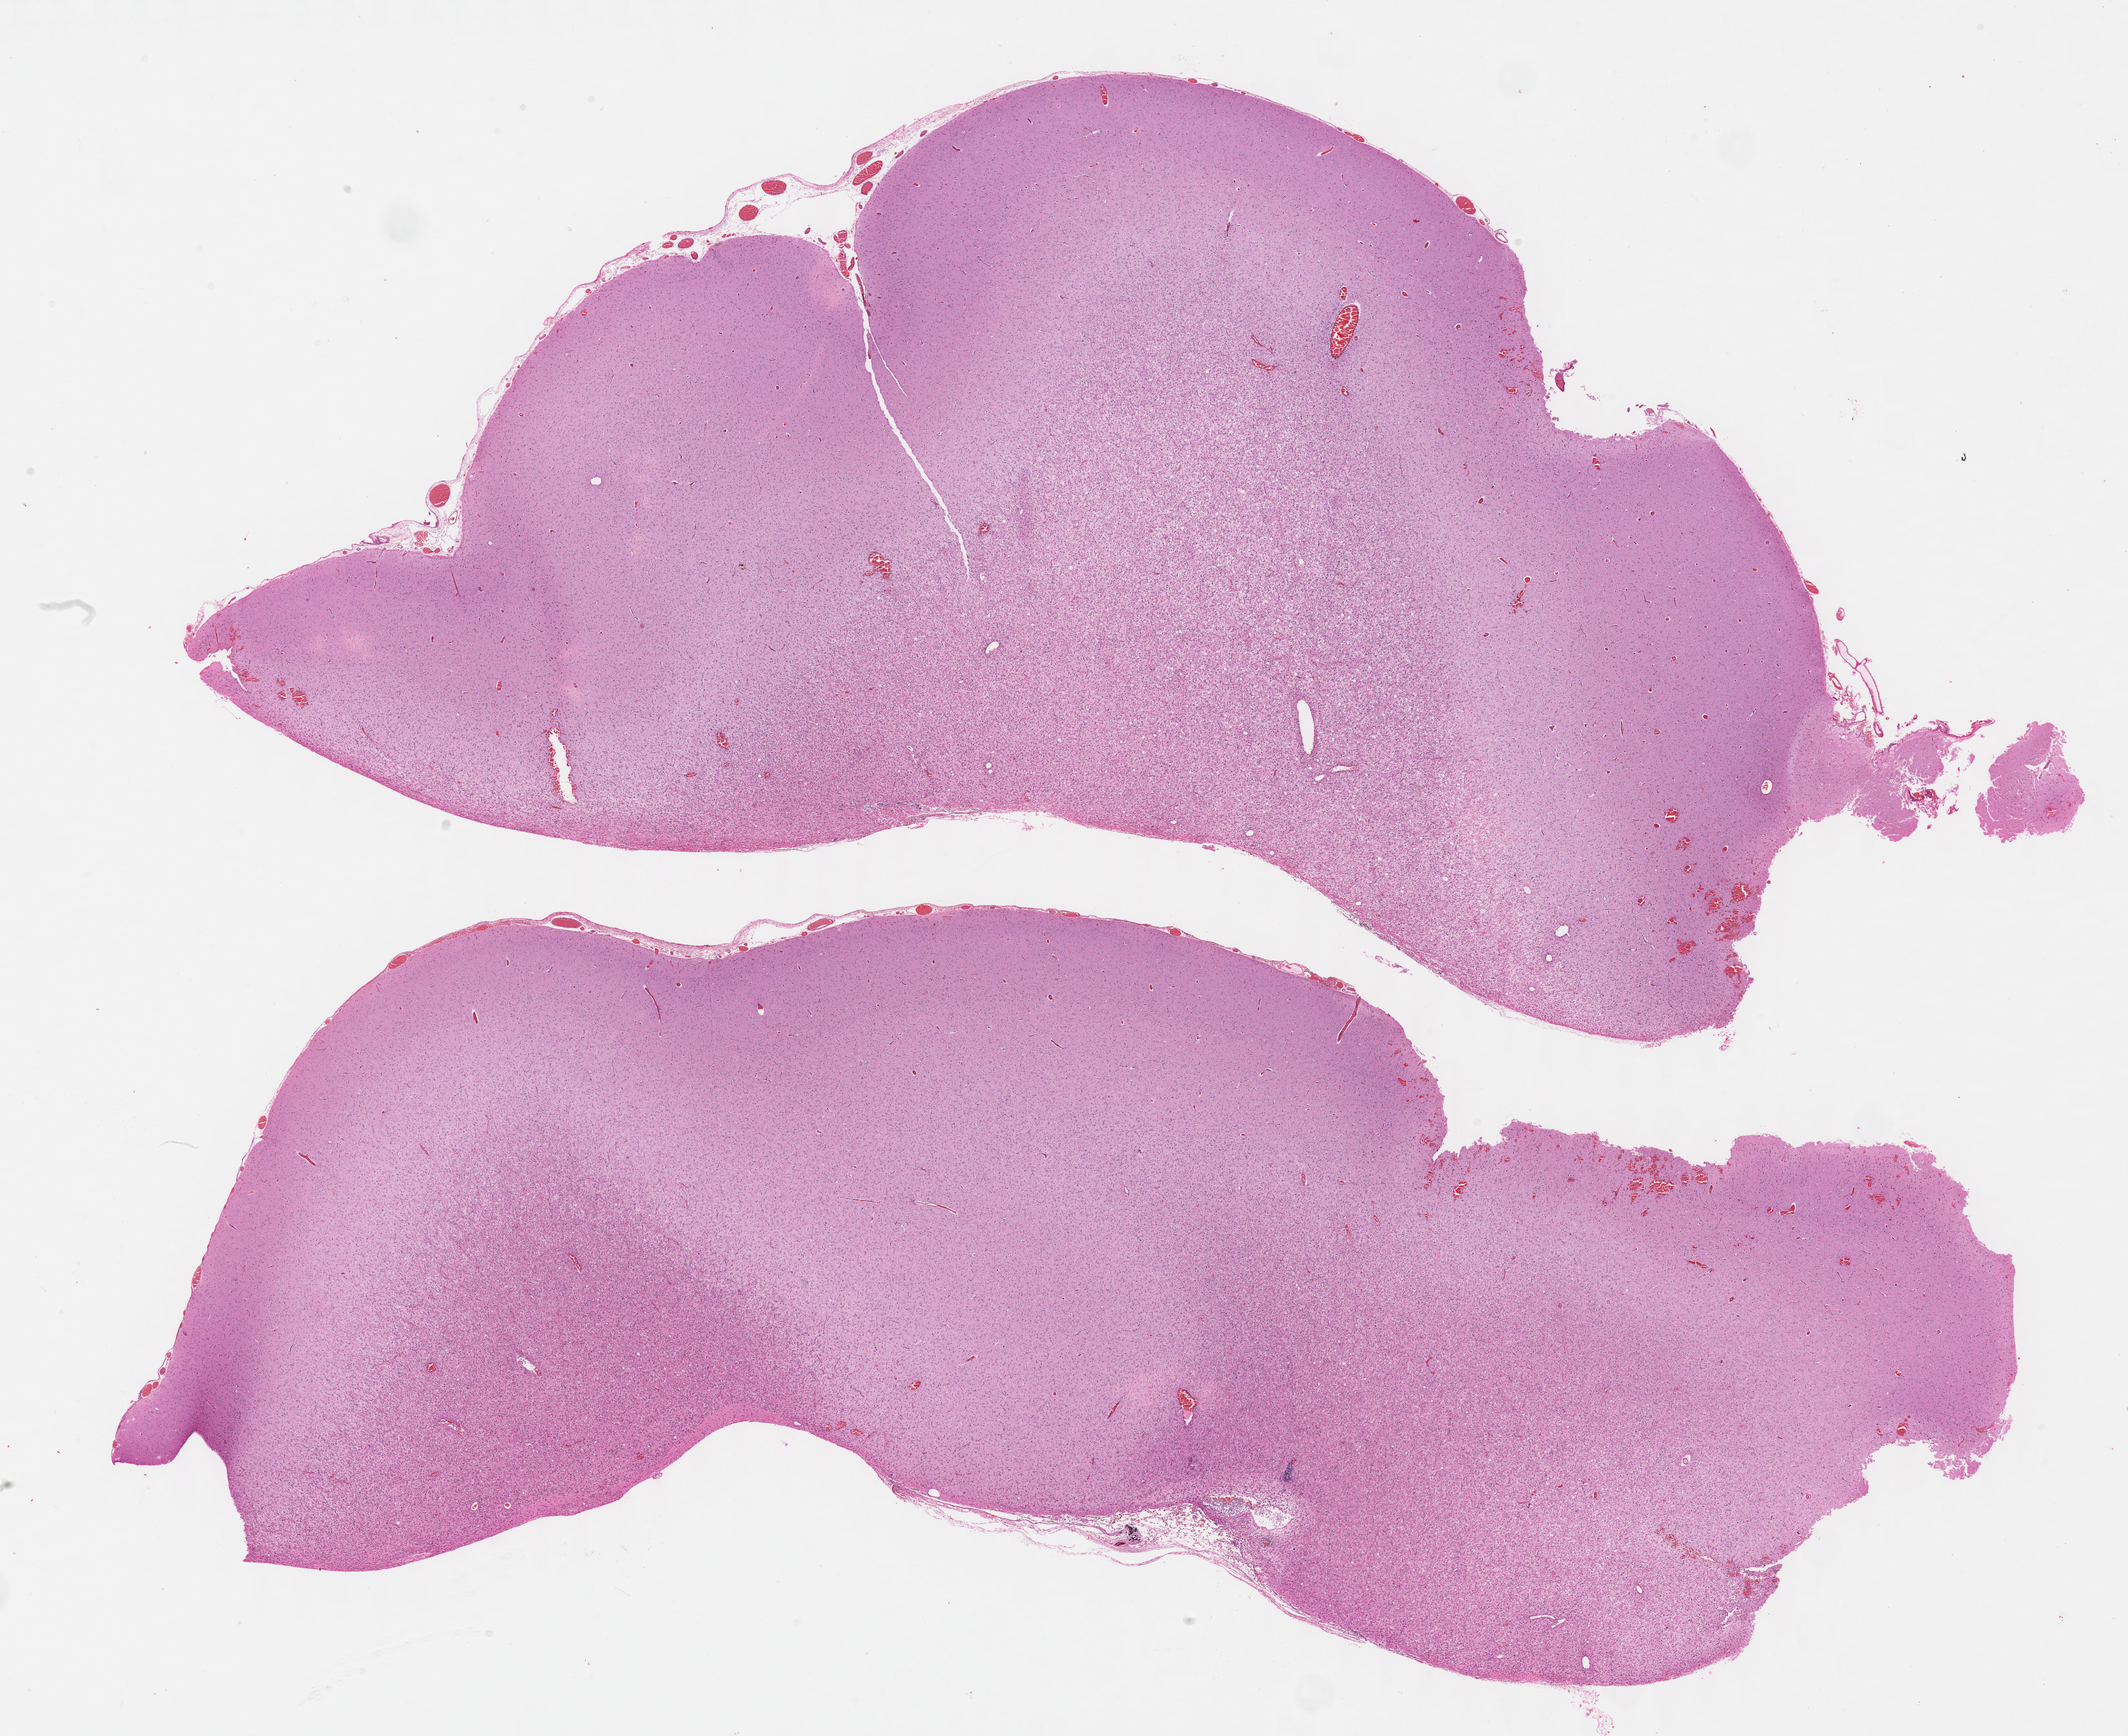
Digitized H&E-stained tissue section (whole slide), whole scanned area (about 26.7 x 21.7 mm) shown as a low-resolution overview, formalin-fixed paraffin-embedded (FFPE) diagnostic section, brain, recurrent tumour sample. Male patient; age at initial diagnosis 29 years.
• this section: recurrent tumour
• patient diagnosis: Oligodendroglioma, NOS (cerebrum)